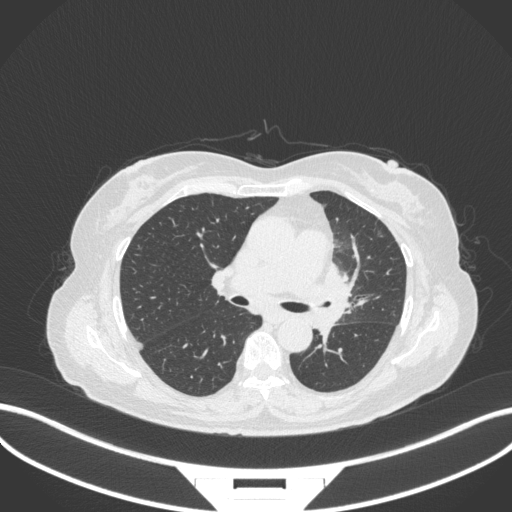
Chest CT, one axial slice; slice 196 of 382 in the series (ordered by position); lung window (W 1500 / L -600 HU); 512 × 512 image matrix, field of view 400 × 400 mm. Female patient, age 64 years. Case-level facts recorded for this patient, not image findings: clinical TNM (as recorded): T2a N2 M0.
Structures marked on this image (bounding box drawn by a radiologist):
- lung tumour (recorded histology: adenocarcinoma): bounding box <318,259,350,338> (left, top, right, bottom; pixels)